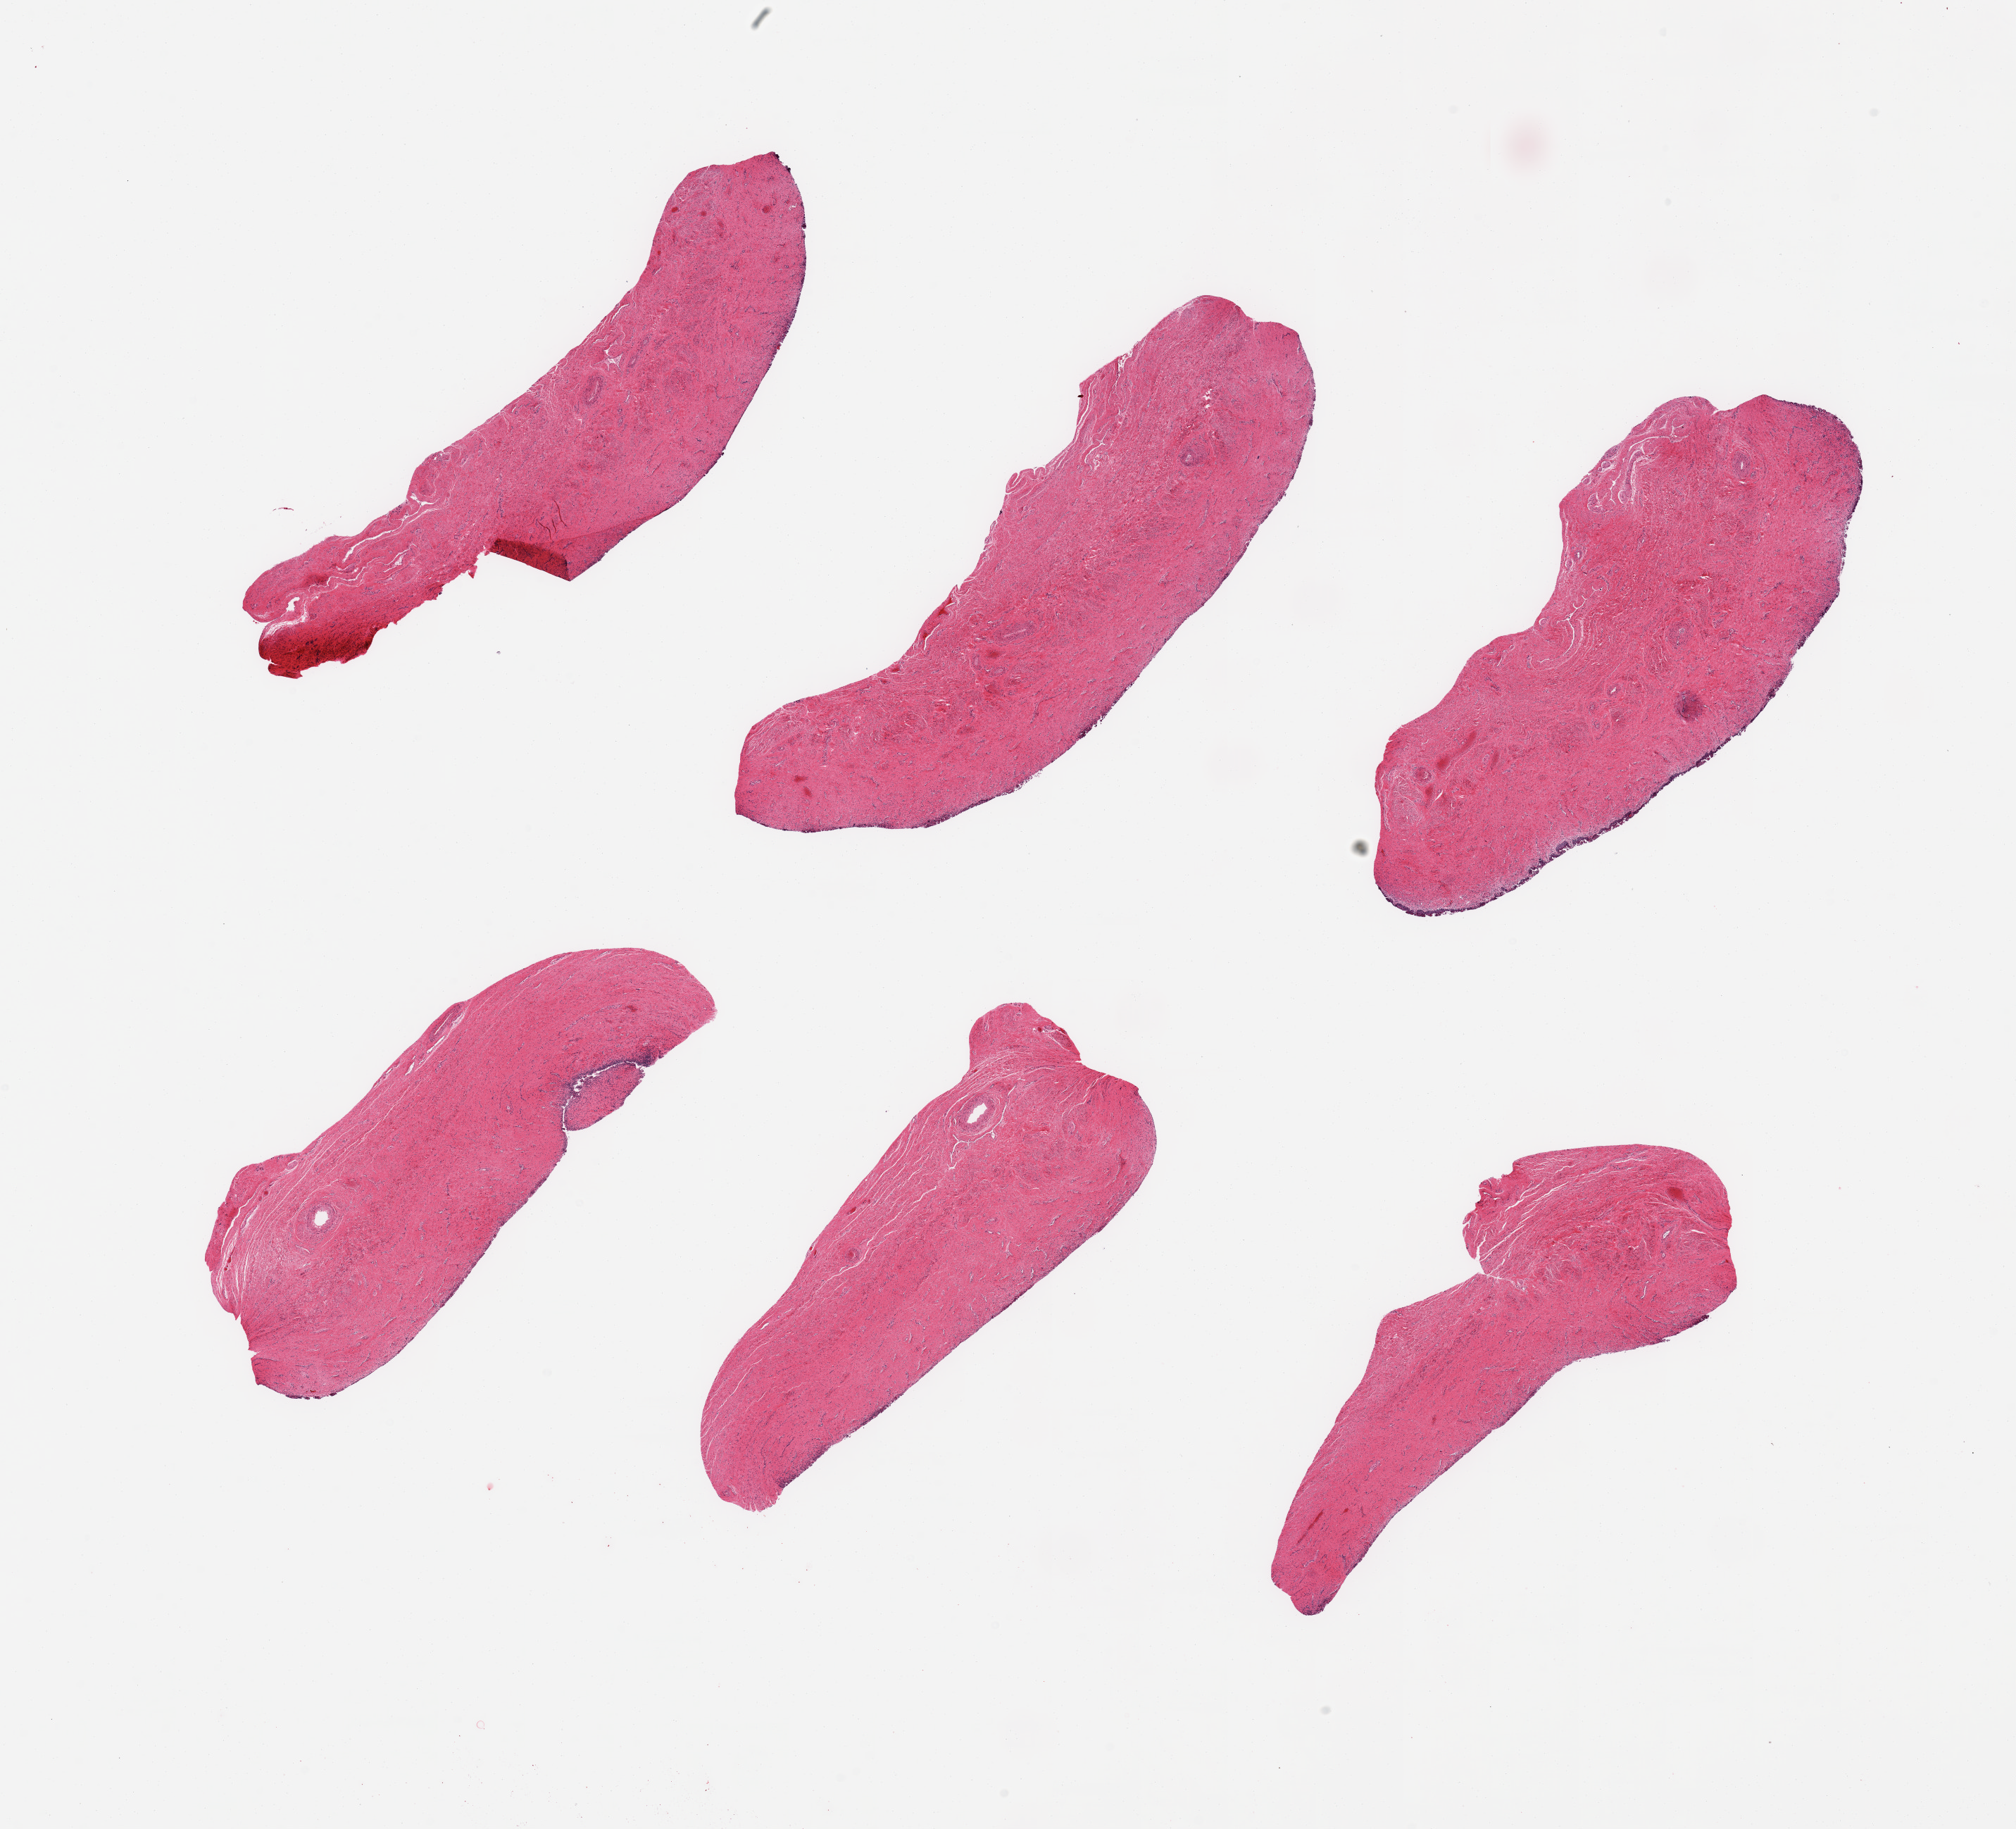
Hematoxylin and eosin (H&E) whole-slide image, brightfield — shown as a low-resolution overview of the whole scanned area (about 22.6 x 20.5 mm); PAXgene-fixed, paraffin-embedded tissue; target tissue: vagina; tissue donor sample. Donor: female.
Reviewer comment on this tissue sample: 6 pieces; epithelium largely sloughed.